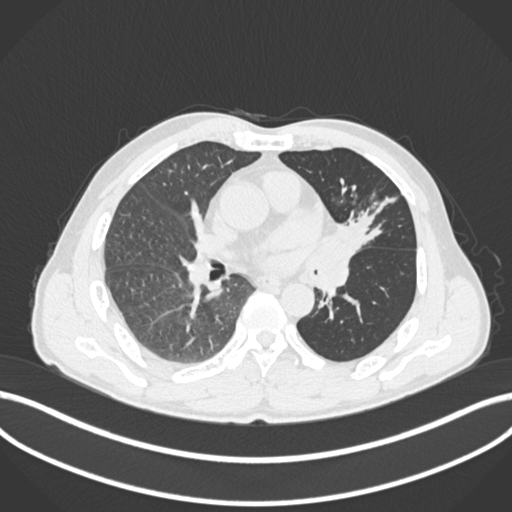
Chest CT, one axial slice; position 96 of 255 along the scan axis; reconstruction kernel B30f; 120 kVp; lung window (W 1500 / L -600 HU); 1 mm slice thickness; 512 × 512 image matrix. Patient: male, 57 years. Case-level facts recorded for this patient, not image findings: clinical TNM (as recorded): T2b N0 M0.
Structures marked on this image (rectangle marked by the reading radiologist):
- lung tumour (recorded histology: squamous cell carcinoma): box from (x=325, y=205) to (x=375, y=273) px